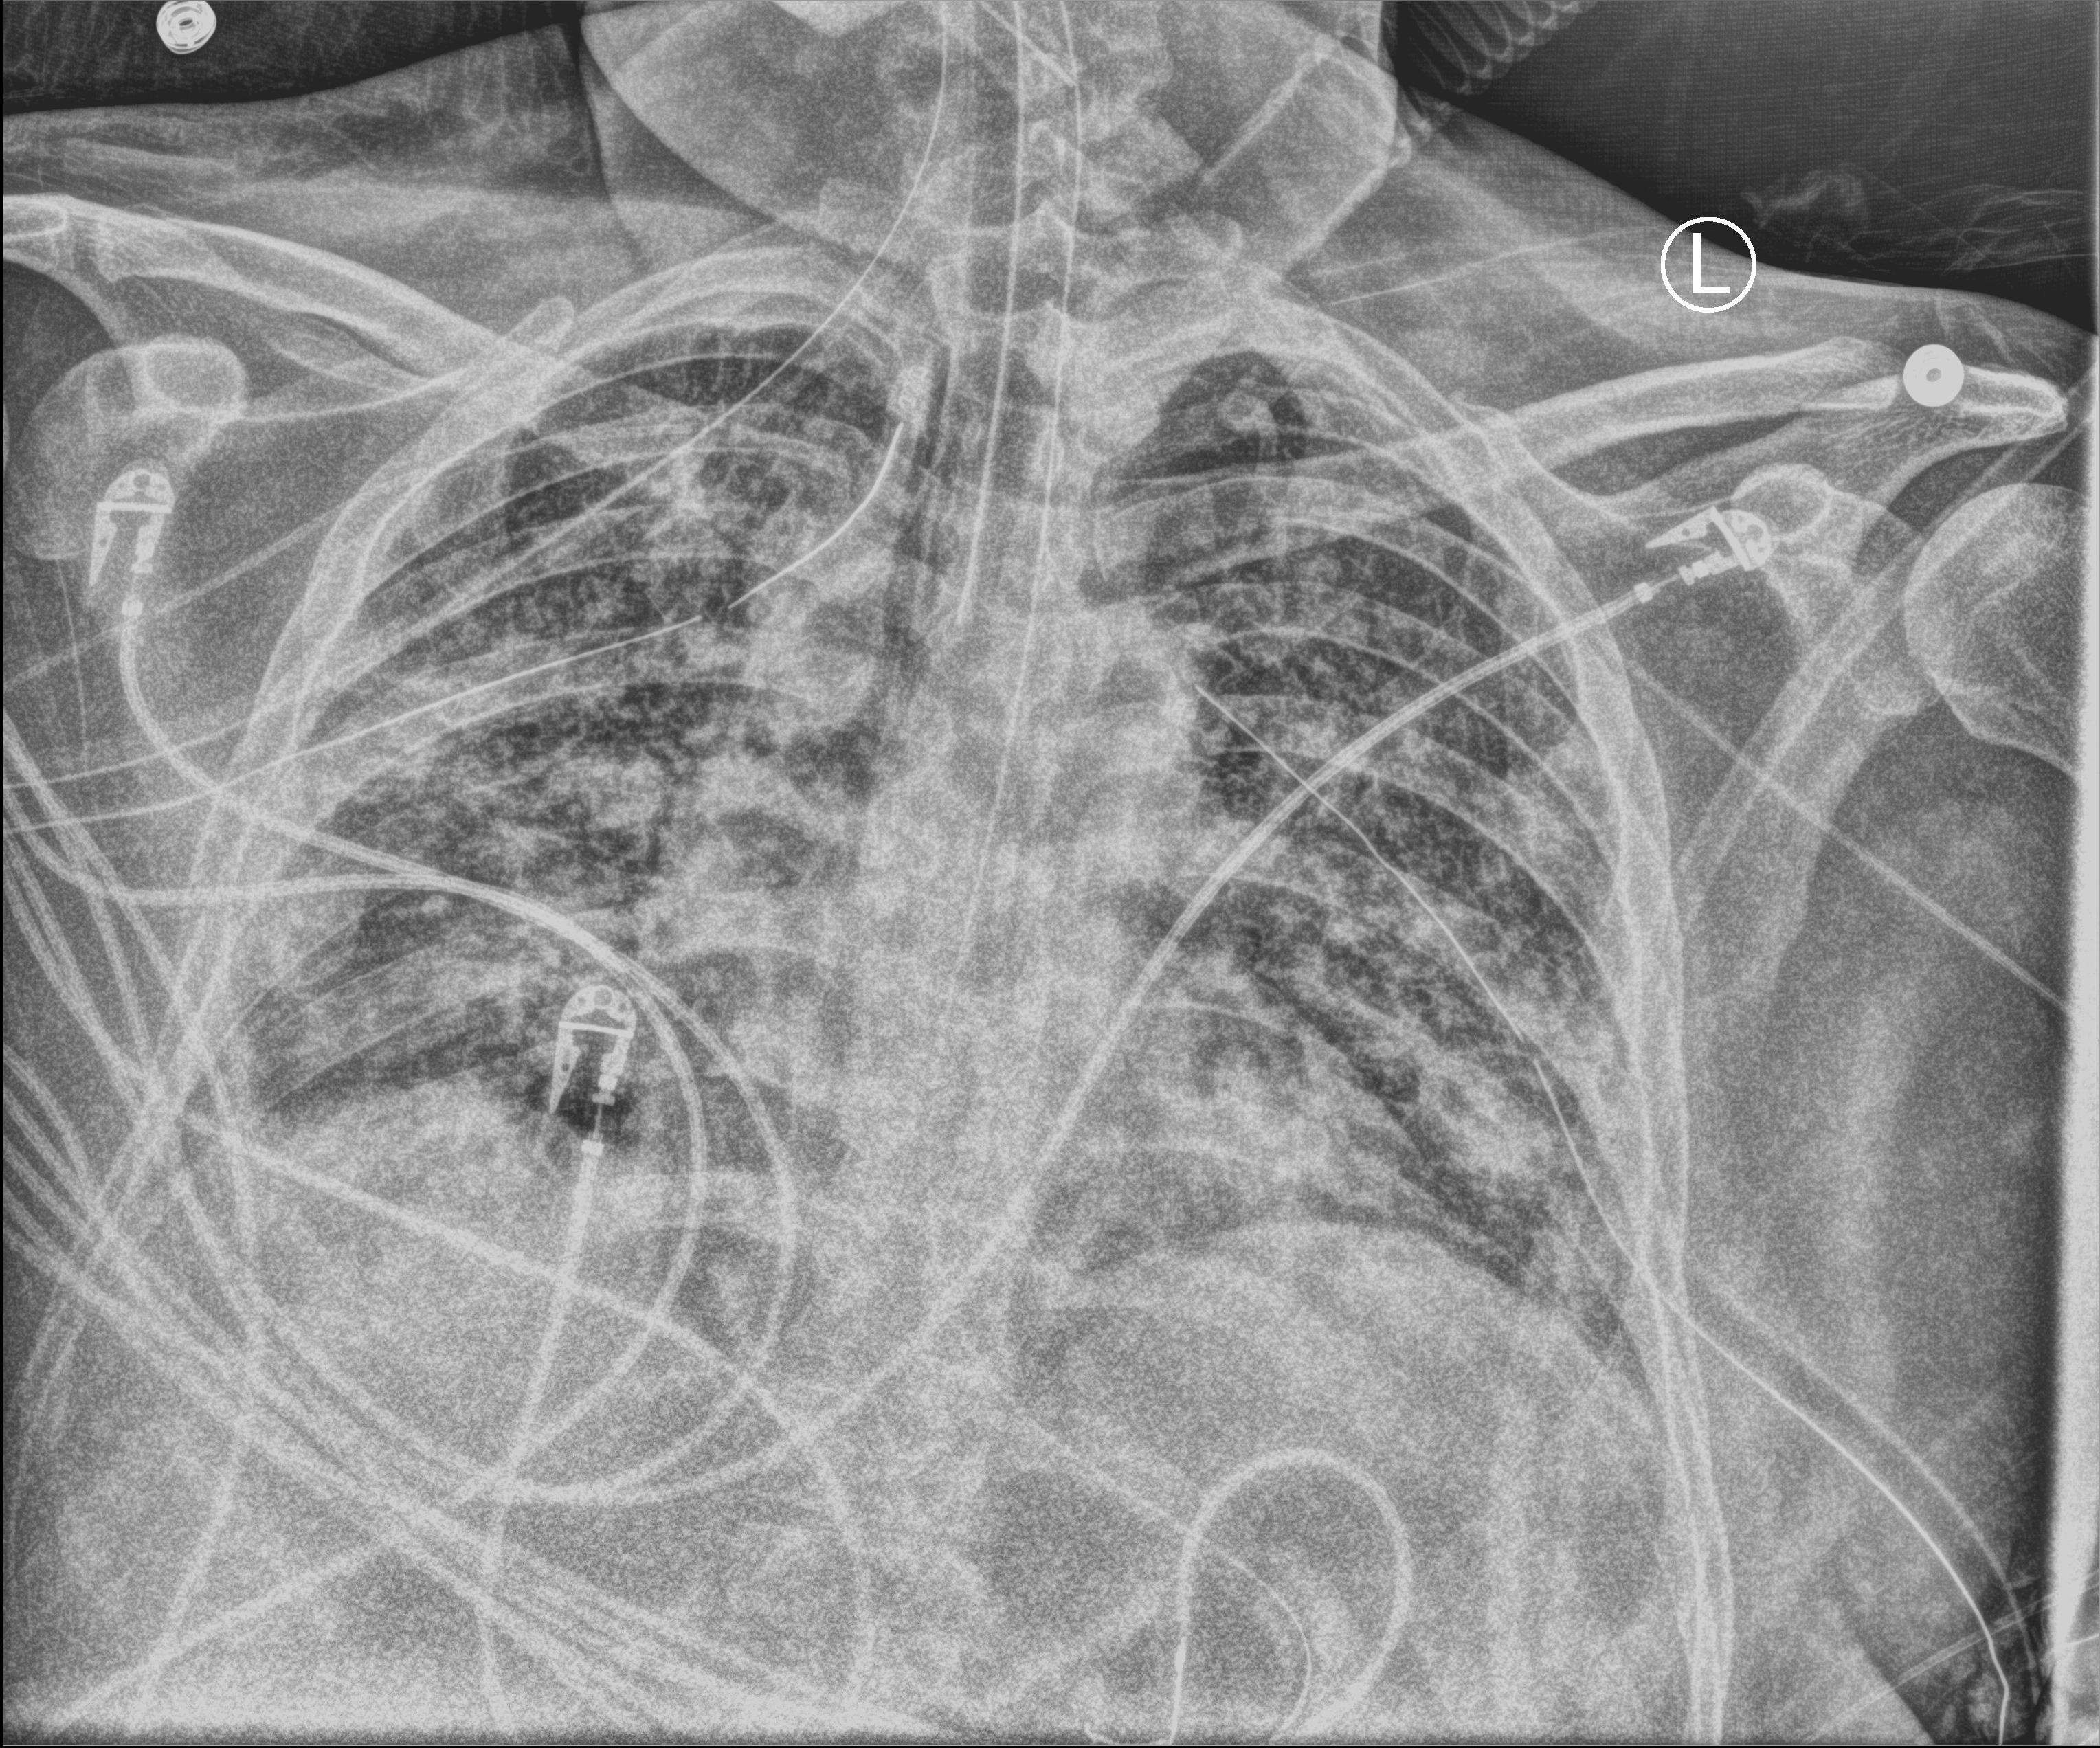
Bedside chest radiograph (computed radiography); anteroposterior (AP) projection. Patient hospitalised with COVID-19; male, aged 18–59 years.
Hospital-stay facts (about this admission, not read from this image; timing relative to this image not recorded):
- admitted to intensive care during this hospital stay: yes
- smoking status (admission record): never
- other chronic lung disease (admission record): no